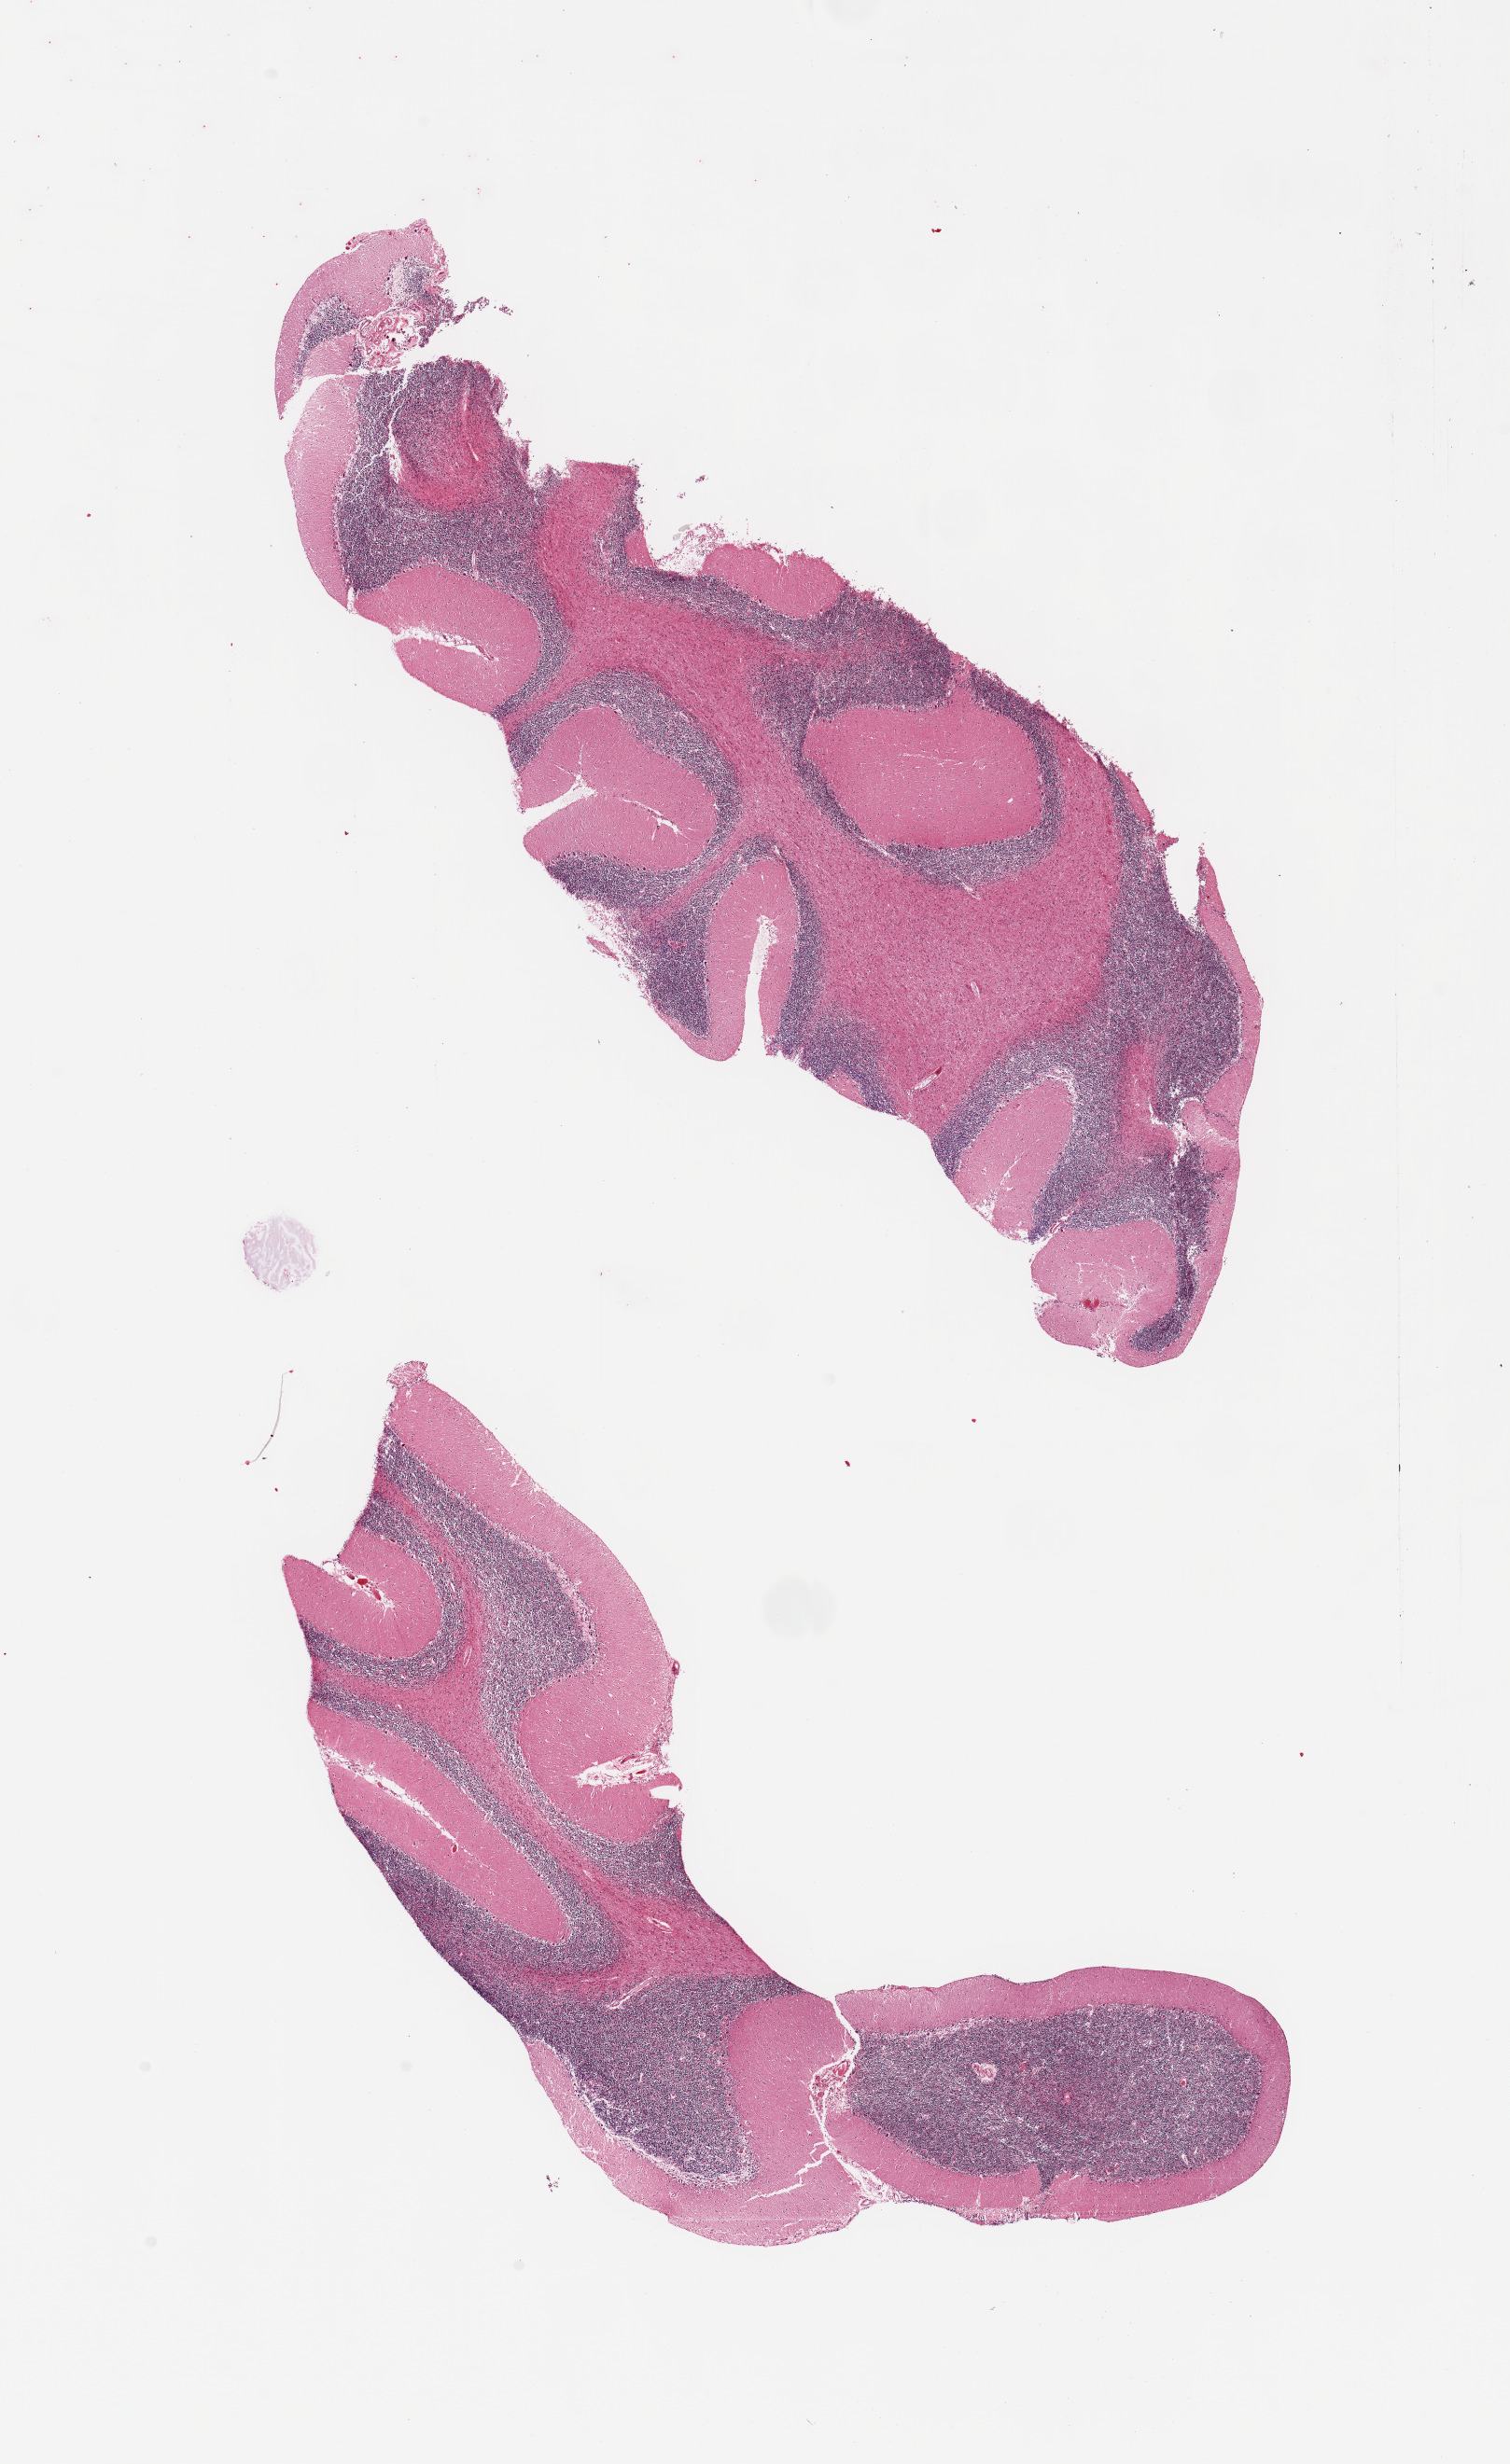
H&E whole-slide image, whole scanned area (about 12.8 x 20.9 mm, from a 20x scan) shown as a low-resolution overview, PAXgene-fixed, paraffin-embedded tissue, section of cerebellum (target tissue), tissue donor sample. Donor: male.
Pathologist's review note for this sample: 2 pieces.